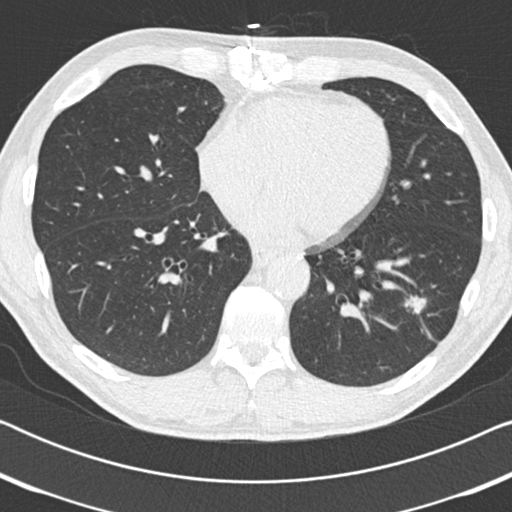
Chest CT (low-dose screening protocol), one axial image; third screening round (two years after baseline); lung window (W 1500 / L -600 HU); 2 mm slice thickness; slice 113 of 186 in the series; 512 × 512 image matrix. Male participant, aged 59 years at enrolment. Current smoker at enrolment.
Lesion marked by an expert reader, bounding box <389,279,455,342> (left, top, right, bottom; pixels). The screening reader recorded 2 non-calcified nodules or masses ≥4 mm on this exam (left lower lobe, right middle lobe); which of them this box marks is not recorded. Later outcome: lung cancer diagnosed 73 days after this screen — adenocarcinoma, NOS, left lower lobe, poorly differentiated (G3), stage IA (AJCC 6th edition), 20 mm at pathology.